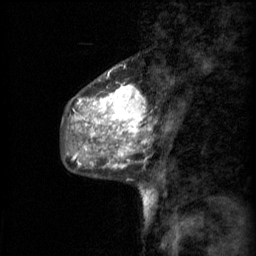
Breast MRI (dynamic contrast-enhanced), one sagittal slice; 3 images stored at this slice position (order not interpretable as contrast timing); 1.5 T; TE 4.2 ms, TR 11 ms; 256 × 256 image matrix. Female patient, age 48 years.
Structures marked on this image (semi-automatically segmented with operator editing):
- analysis volume of interest (the breast-tissue region the enhancement analysis was run in; not a lesion): box from (x=69, y=74) to (x=148, y=147) px
- tumour enhancement mask (voxels above the 70 % enhancement threshold inside the analysis volume of interest): (x=75, y=74)–(x=144, y=147)